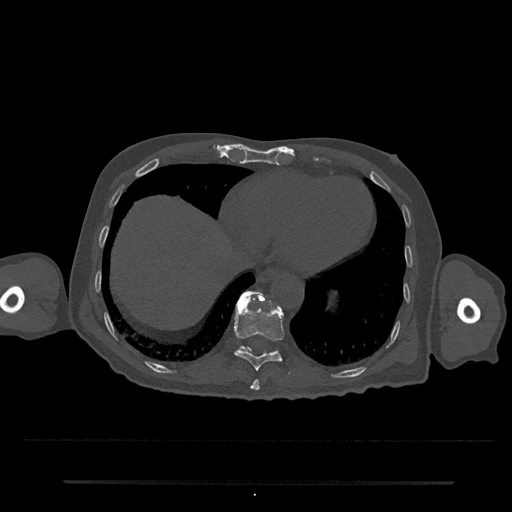
CT including the spine, one axial slice; bone window (W 1800 / L 400 HU); 0.5 mm slice thickness; 512 × 512 image matrix, field of view 427 × 427 mm. Male patient, age 74 years. Case-level facts recorded for this patient, not image findings: primary cancer: prostate.
Structures marked on this image (semi-automatically segmented with operator editing):
- T10 vertebra: box from (x=234, y=293) to (x=291, y=374) px
- T11 vertebra: (x=236, y=291)–(x=263, y=352)
- T9 vertebra: (x=250, y=379)–(x=260, y=391)